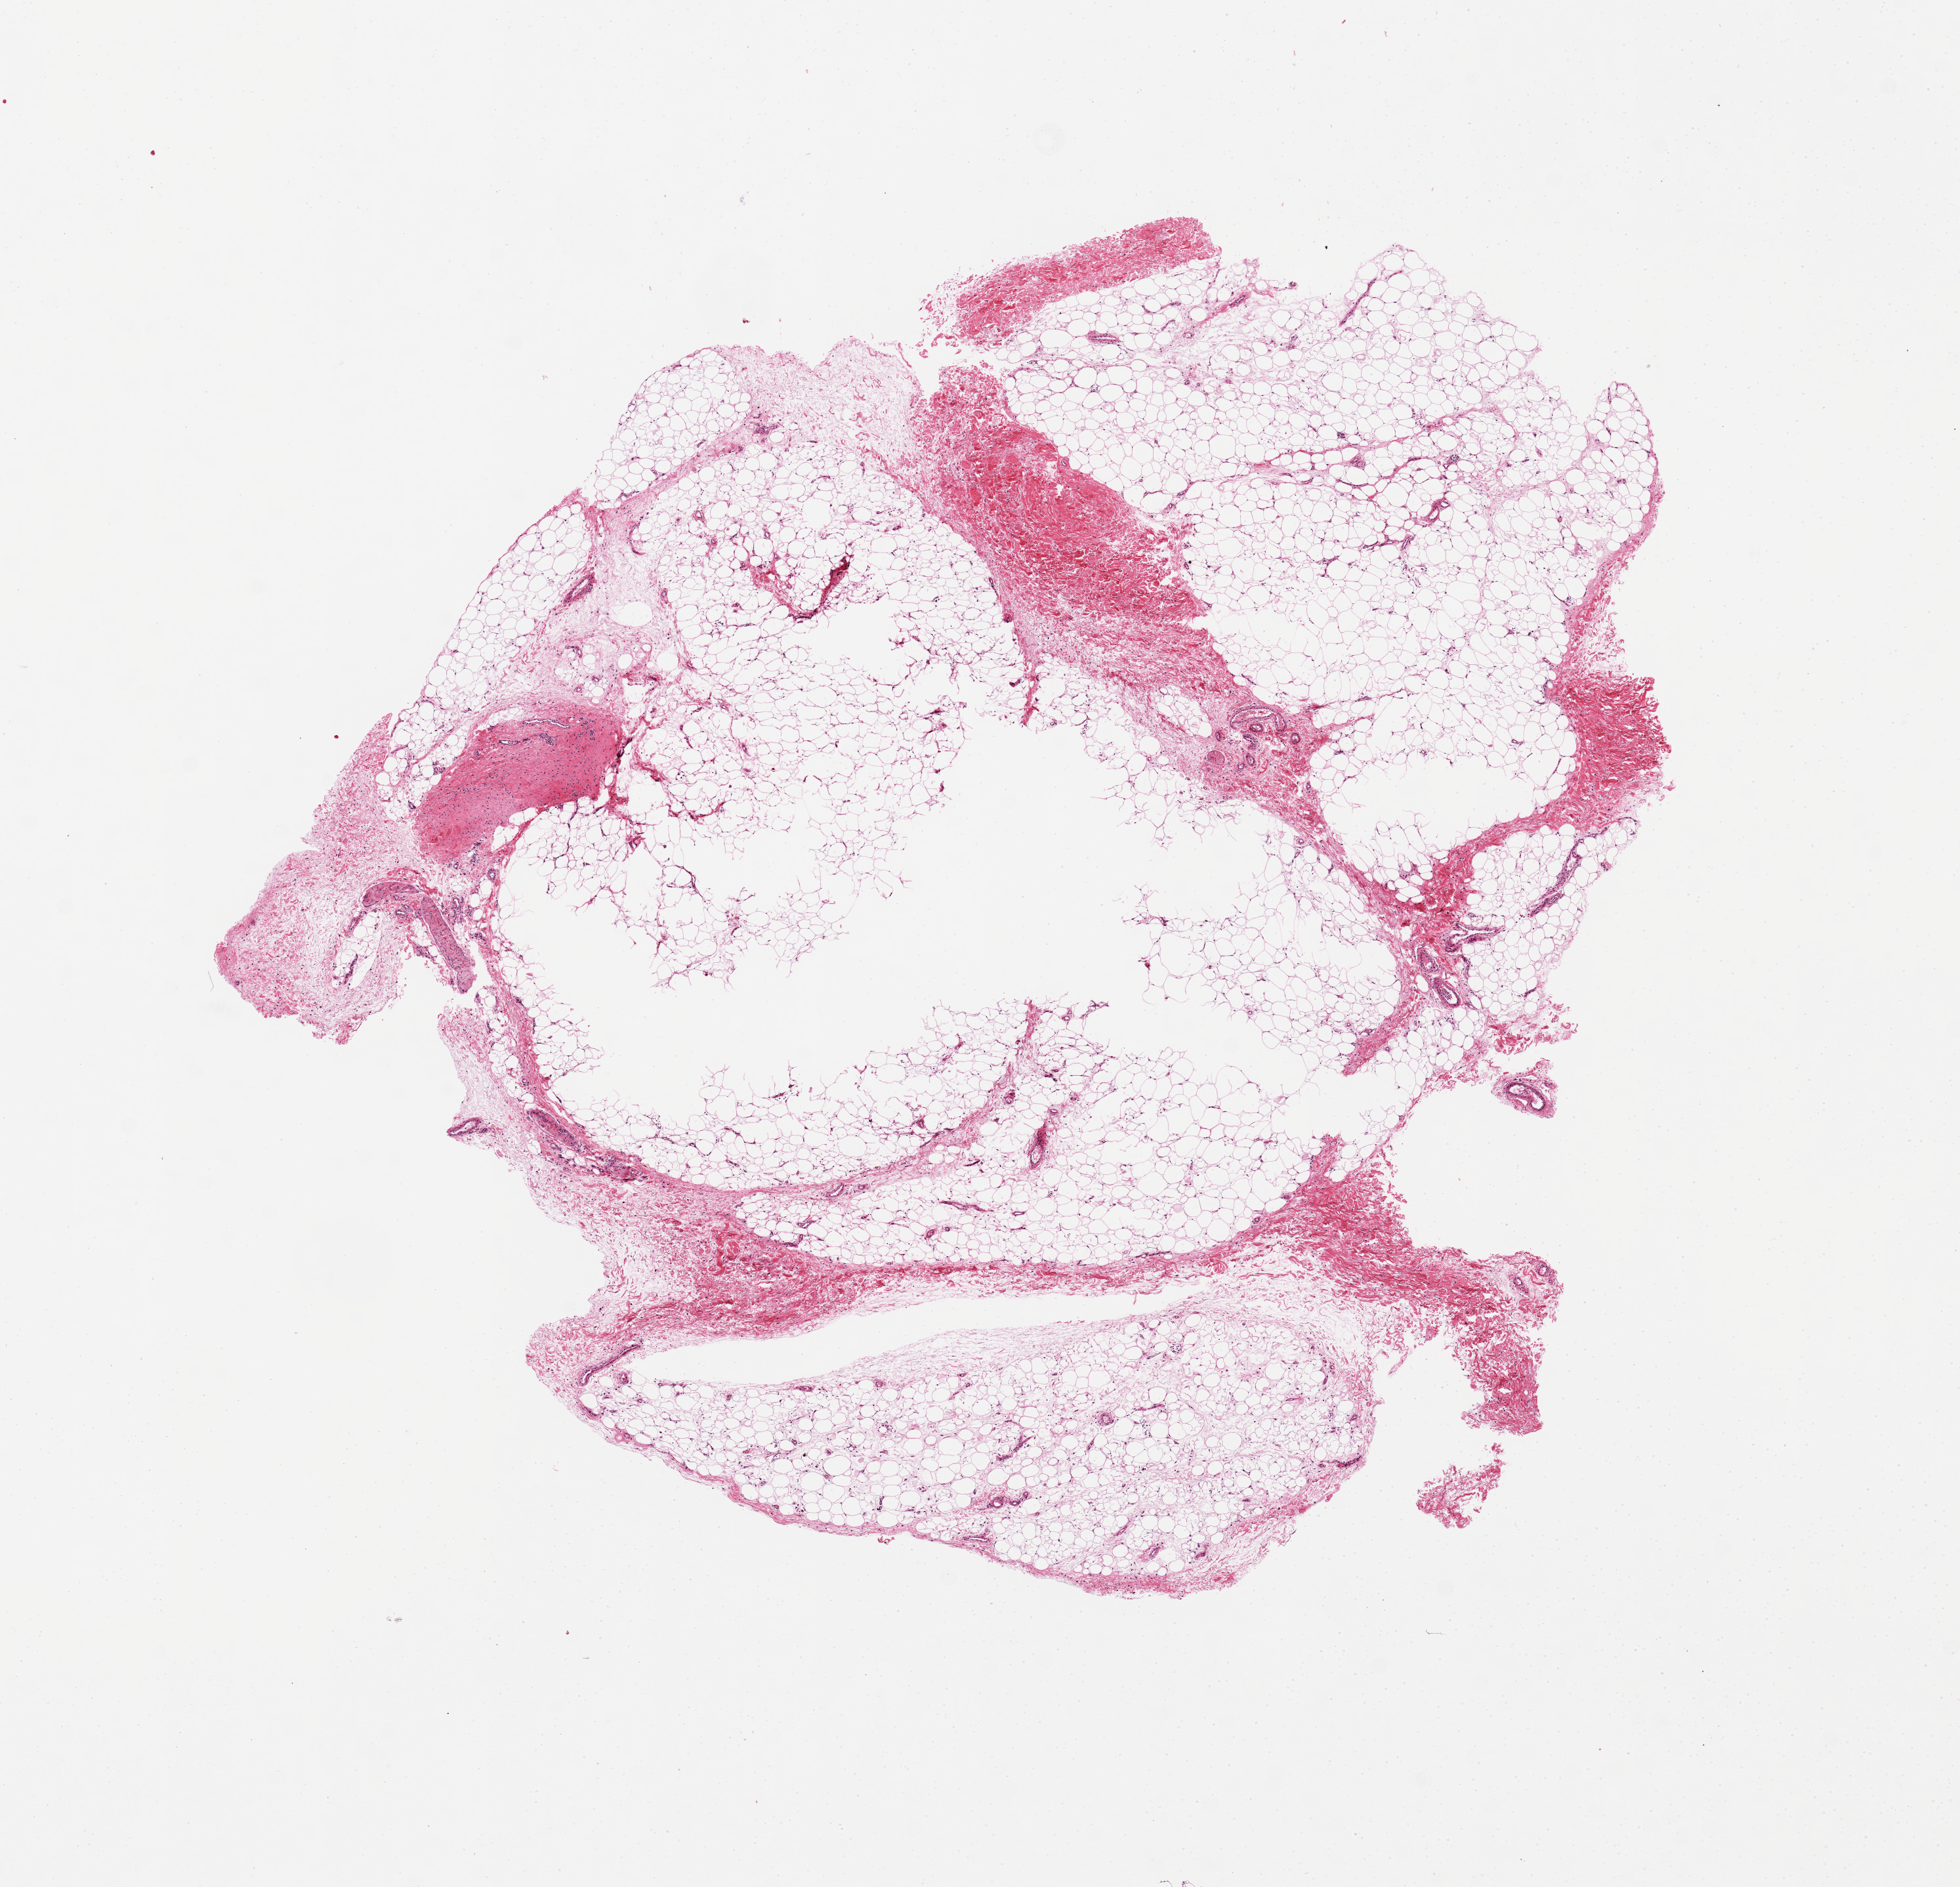
Whole-slide image, haematoxylin and eosin stain — a low-resolution overview of the entire scanned area, about 11.8 x 11.4 mm; PAXgene-fixed paraffin-embedded (PFPE) section; target tissue: adipose tissue; donor tissue sample. Donor: male.
Review note (as recorded): Central 30% unfixed zone.